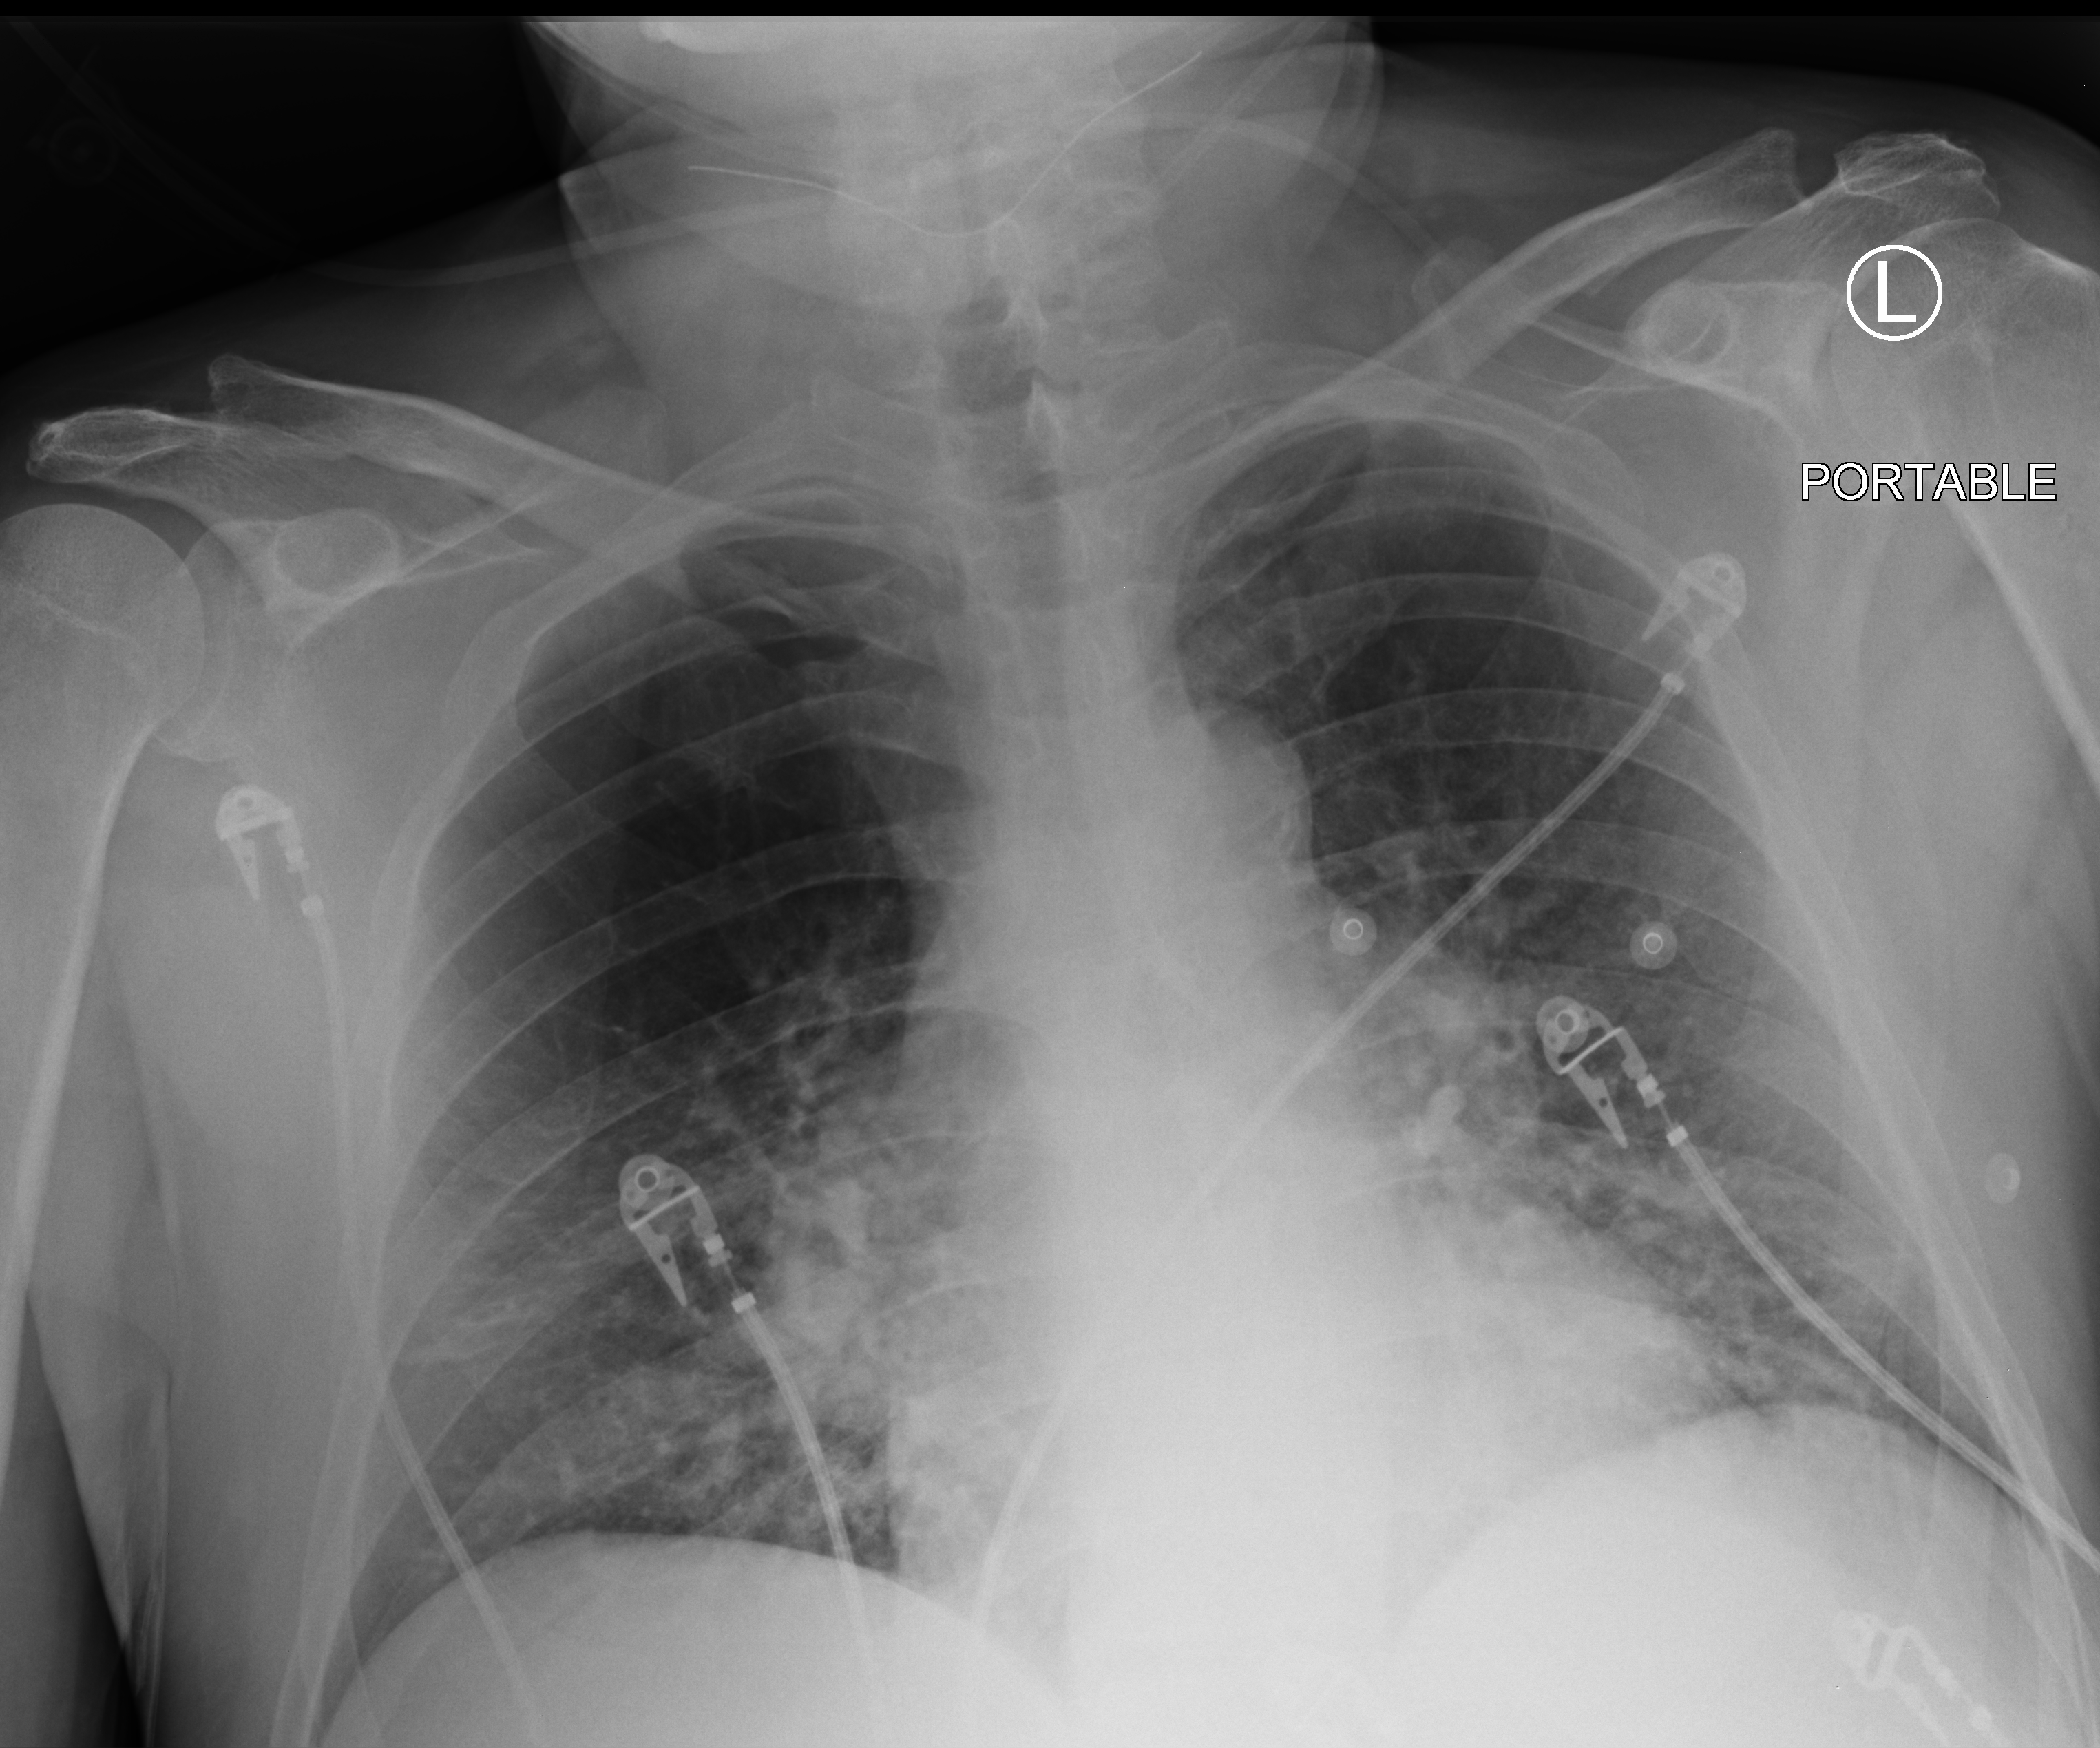
Portable chest radiograph. Male patient hospitalised with COVID-19, age 18–59 years.
From the hospital-stay record, not from the radiograph (when in the stay this image was taken is not recorded):
- chronic kidney disease (admission record): no